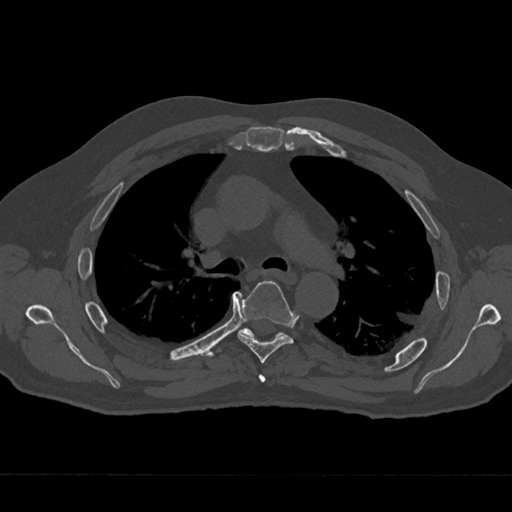
CT including the spine, one axial slice; reconstruction kernel Br40s/3; 120 kVp; bone window (W 1800 / L 400 HU); 0.5 mm slice thickness; 512 × 512 image matrix, field of view 377 × 377 mm. Patient: male, 75 years. Case-level facts recorded for this patient, not image findings: primary cancer: renal; vertebrae with lytic lesions (as recorded): T4.
Structures marked on this image (semi-automatic segmentation, software-assisted and operator-edited):
- T4 vertebra: bounding box [x1, y1, x2, y2] px = [258, 374, 266, 382]
- T5 vertebra: [238, 281, 294, 363]
- T6 vertebra: [239, 328, 283, 337]